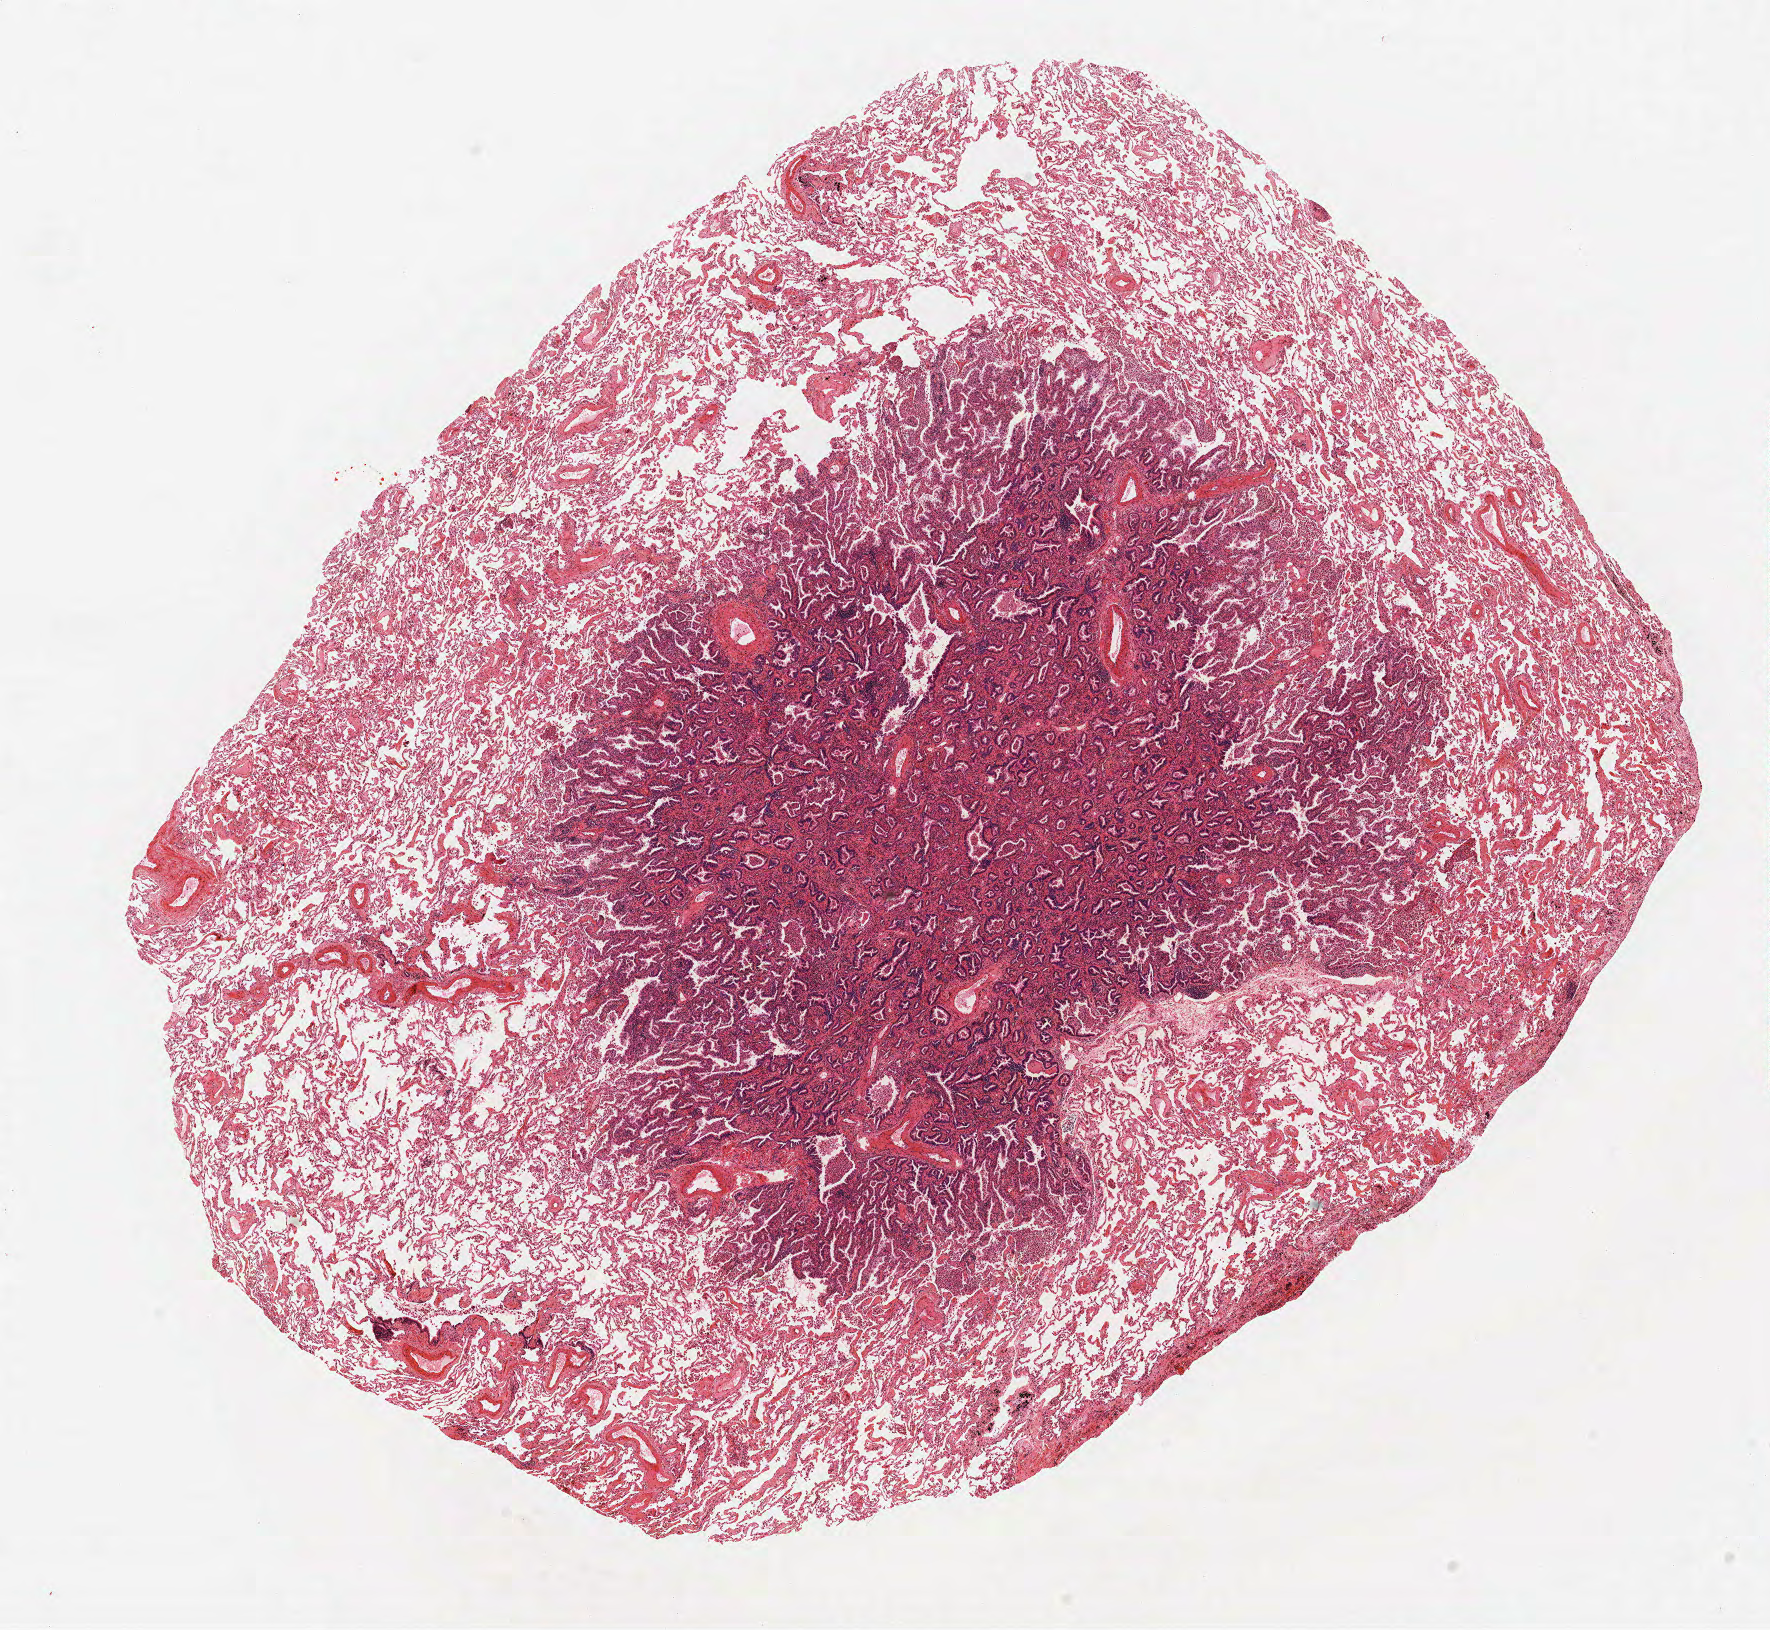
Hematoxylin and eosin (H&E) stained whole-slide image, whole scanned area (about 14.2 x 13.0 mm) shown as a low-resolution overview. Formalin-fixed paraffin-embedded (FFPE) section. Lung tissue. Male patient, aged 62 at enrolment. Former smoker at enrolment. Grade: moderately differentiated (G2).
* primary tumour location (clinical record): left lower lobe
* tumour size (pathology): 58 mm
* ICD-O-3 topography: lower lobe of lung (C34.3)
* stage (AJCC 6th edition): IIIB
* participant's lung-cancer diagnosis: Bronchiolo-alveolar adenocarcinoma, NOS (ICD-O-3 8250/3)